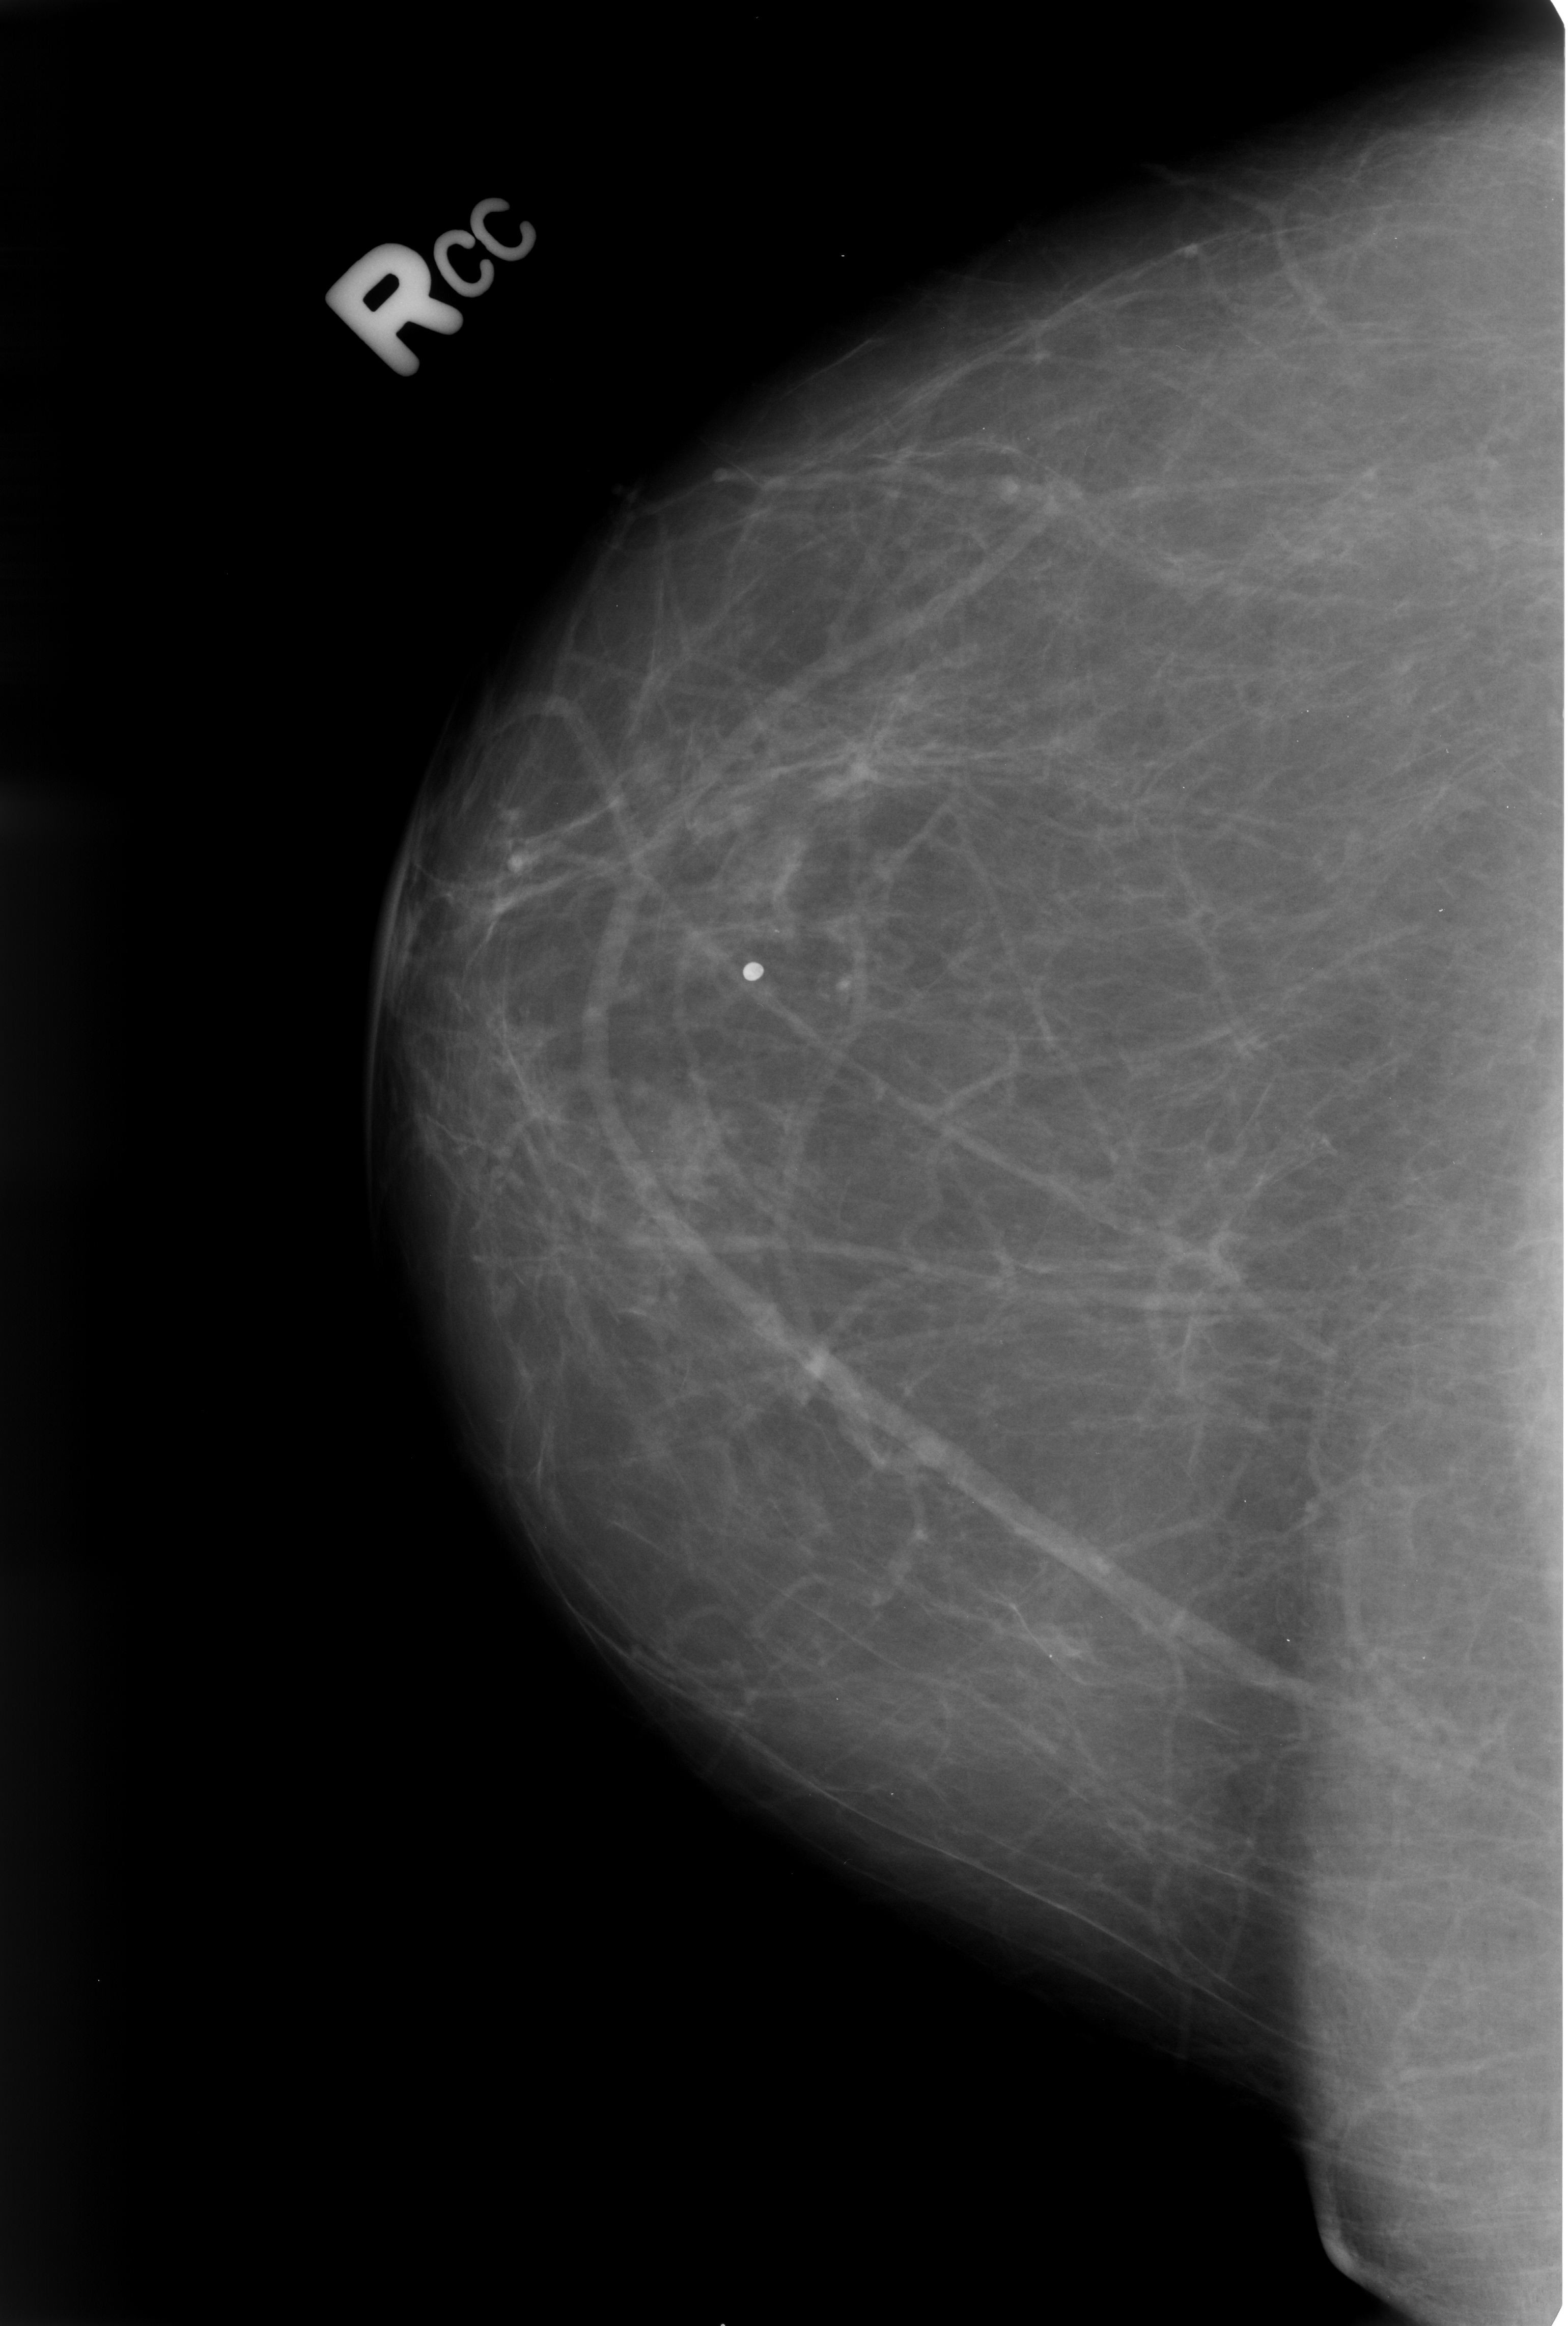
Scanned film-screen mammogram; right breast; CC view; breast composition: scattered fibroglandular densities (BI-RADS density category 2 of 4).
Radiologist-marked abnormalities on this image: calcifications, morphology lucent center; BI-RADS assessment category 2; subtlety rating 5 on a 1 (subtle) to 5 (obvious) scale; benign; no additional work-up was recommended (benign without callback).